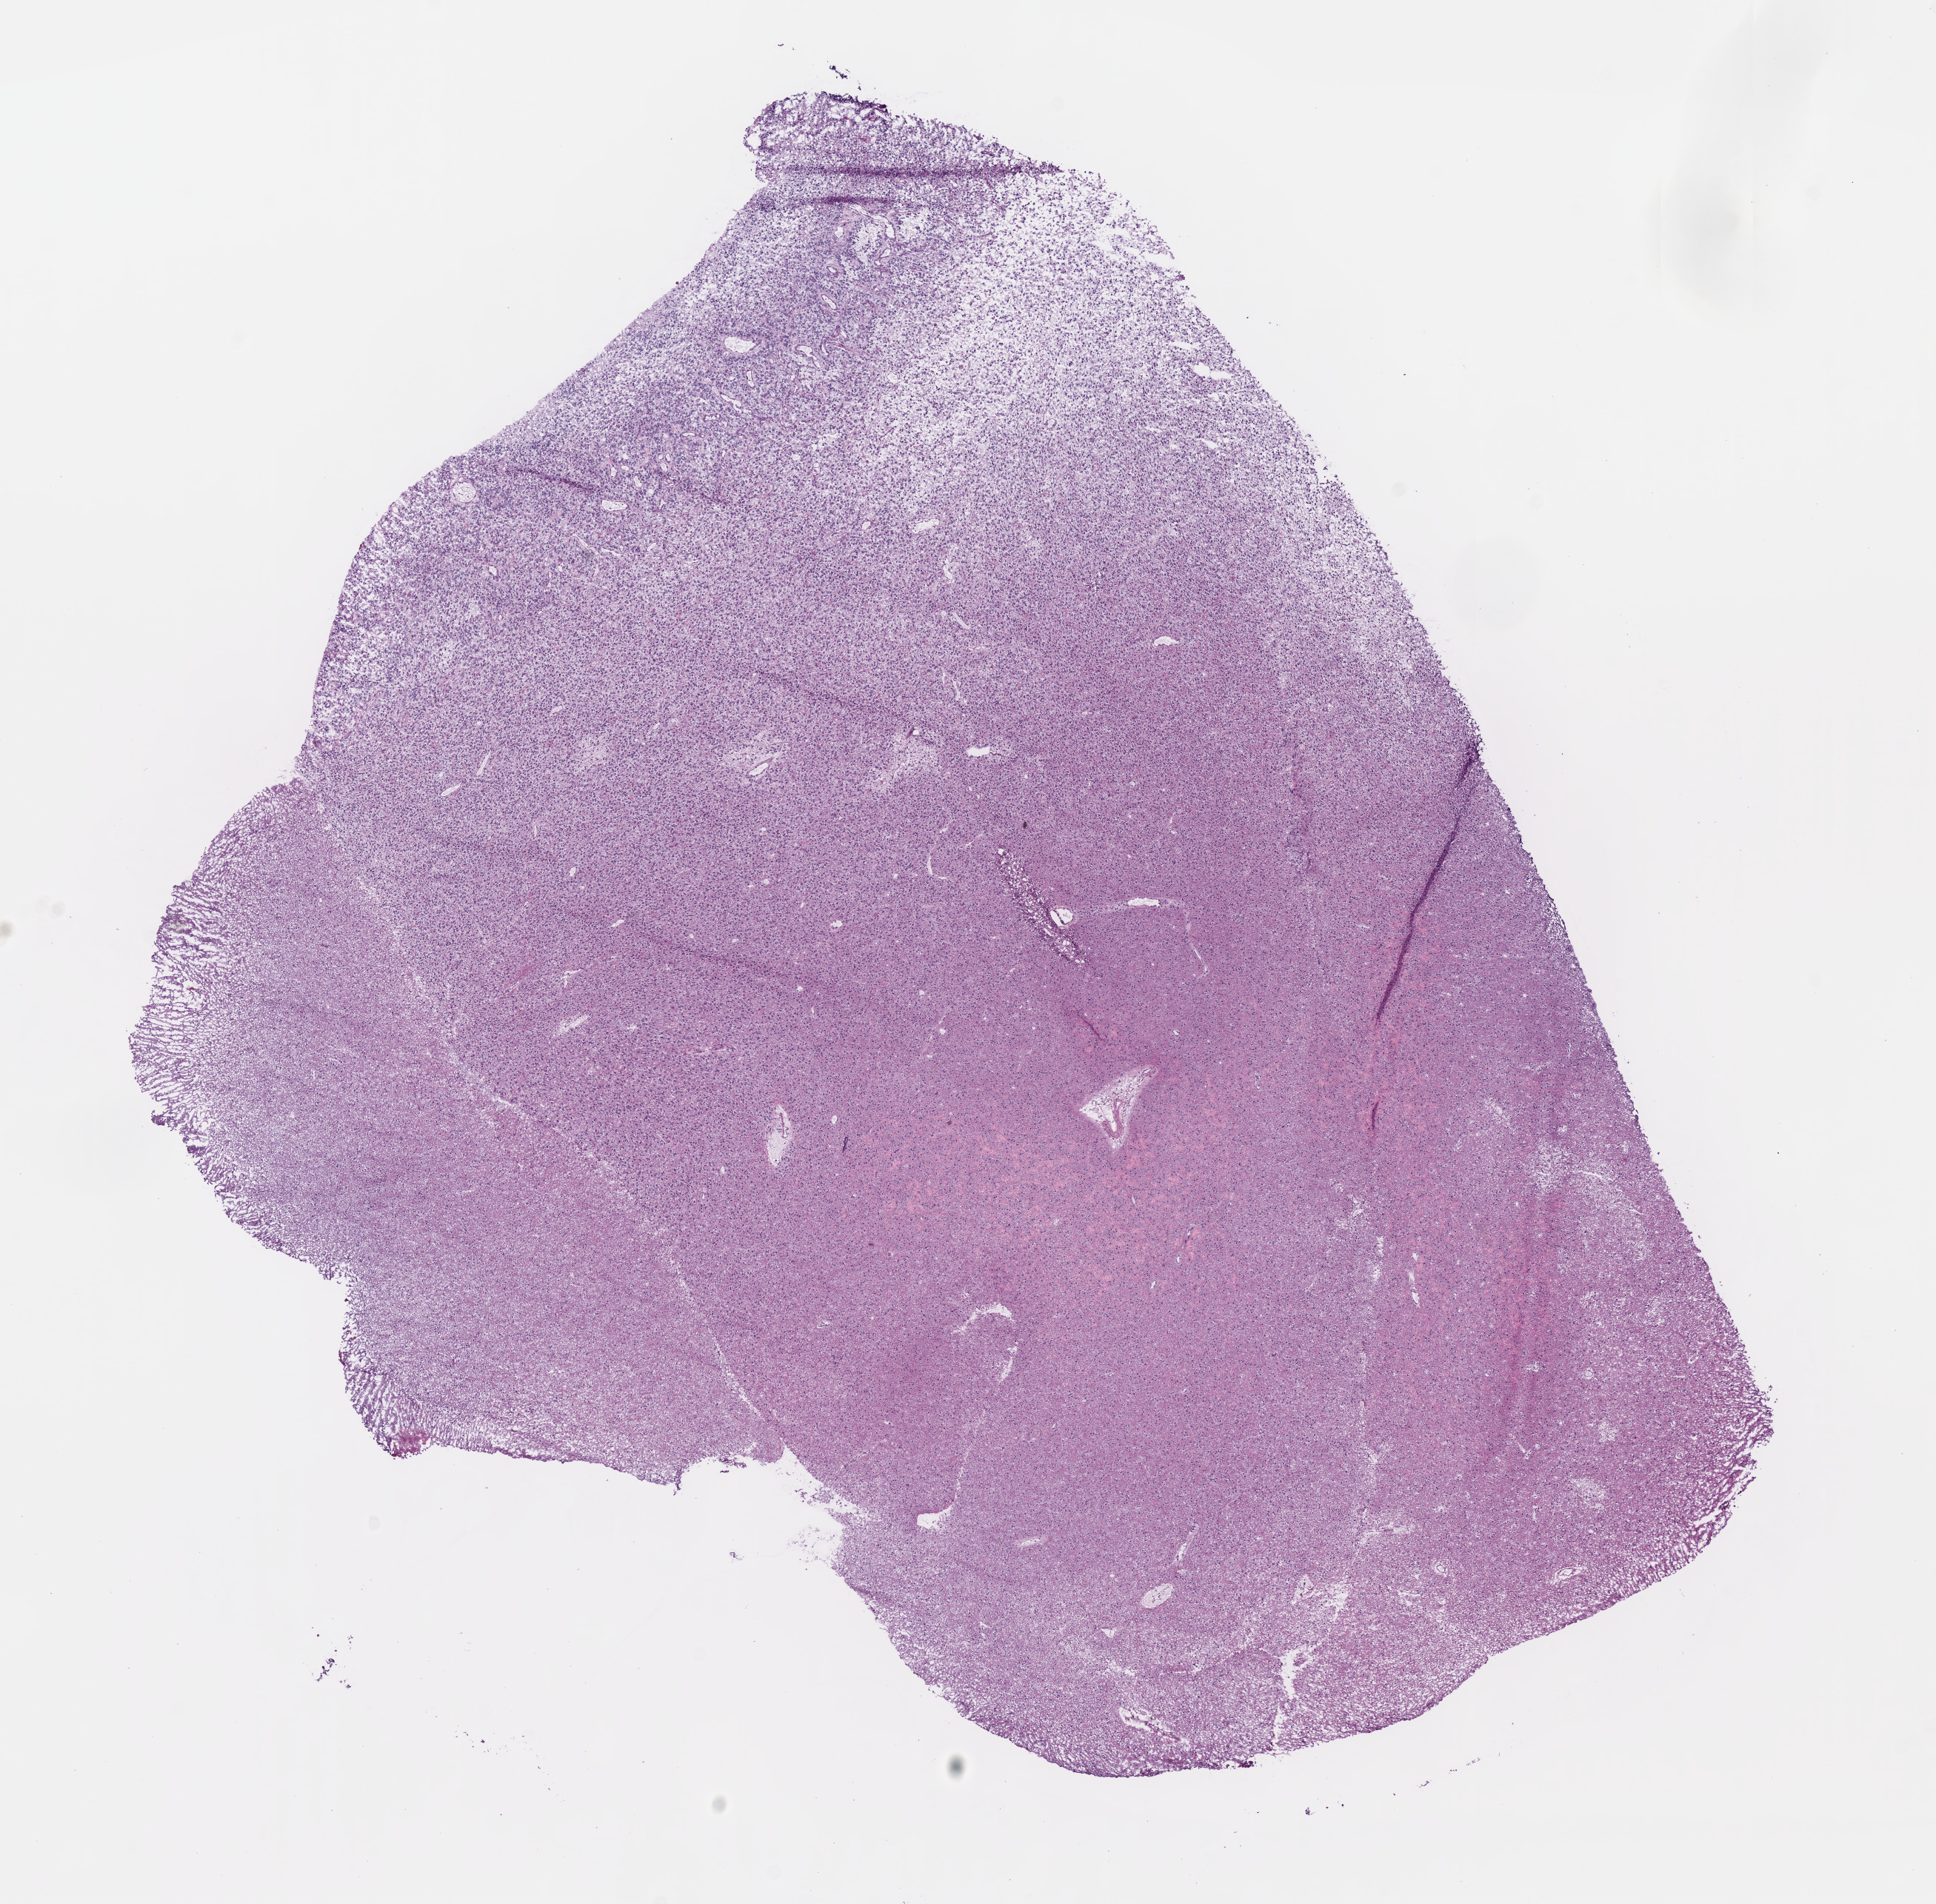
Whole-slide histology image, Hematoxylin and eosin (H&E) stained — a low-resolution overview of the entire scanned area, about 10.3 x 10.1 mm, frozen section from the bottom of the tissue portion, sample: primary tumour, brain. Male, age 28 years at initial diagnosis. Histologic grade: G2 (moderately differentiated). Composition of this section per pathologist review: tumour cells 100%, tumour nuclei 85%, normal cells 0%, stromal cells 0%, necrosis 0%.
* histologic diagnosis: Oligodendroglioma, NOS